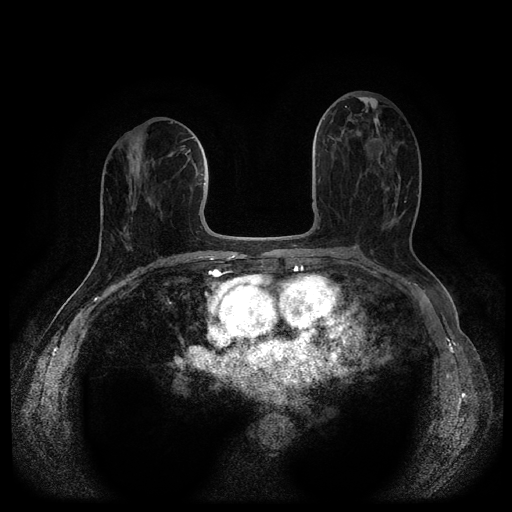
Breast MRI (dynamic contrast-enhanced, multi-phase), one axial slice; position 49 of 116 along the scan axis; dynamic contrast-enhanced series, time point 2 of 5 at this slice position (early post-contrast); 1.5 T; TE 2.6 ms, TR 5.4 ms; 512 × 512 image matrix, field of view 340 × 340 mm. Female patient, age 69 years.
Outlined on this slice (semi-automatically segmented with operator editing):
- breast lesion (labelled benign in the annotation): bounding box [x1, y1, x2, y2] px = [365, 138, 386, 163]